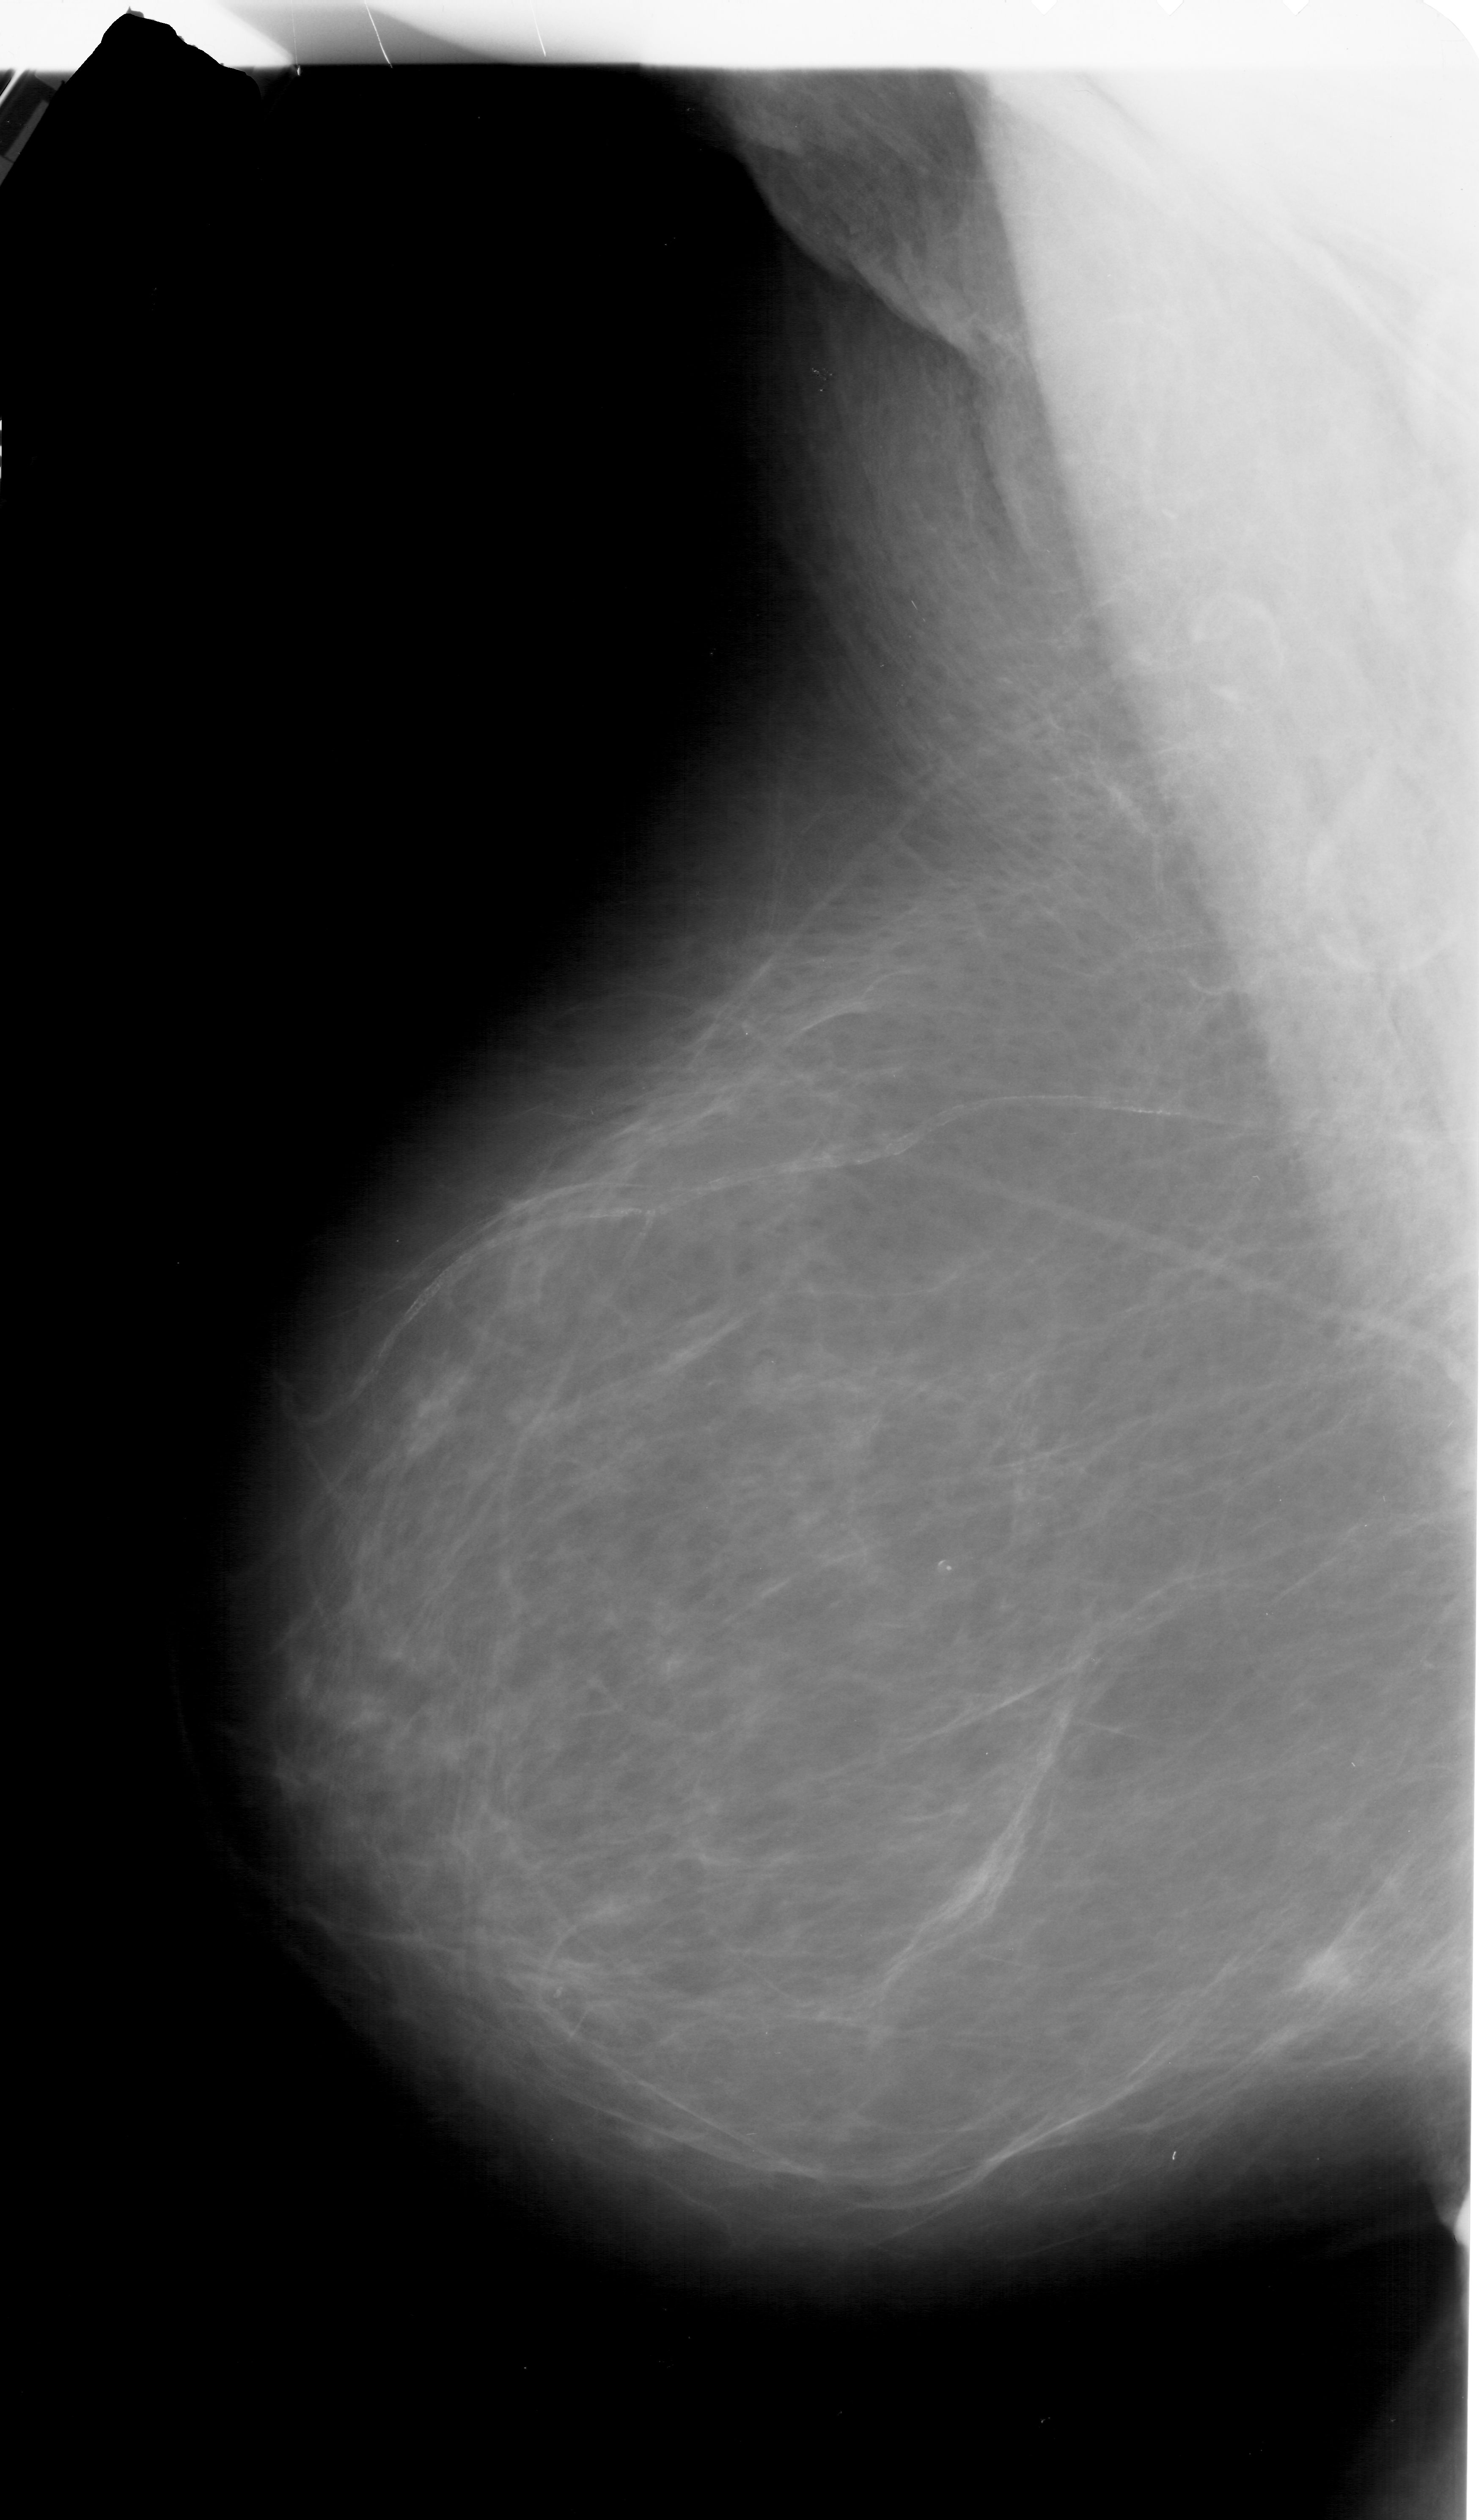
Digitized screen-film mammogram. Left breast. Mediolateral oblique (MLO) view. 1479 × 2520 image matrix.
Expert-marked regions of interest on this image (one box per marked abnormality):
- mass, shape irregular, margins ill defined; BI-RADS assessment category 4; subtlety rating 2 on a 1 (subtle) to 5 (obvious) scale; pathology result (as recorded, not read from the image): malignant: bounding box <1277,1932,1361,2012> (left, top, right, bottom; pixels)